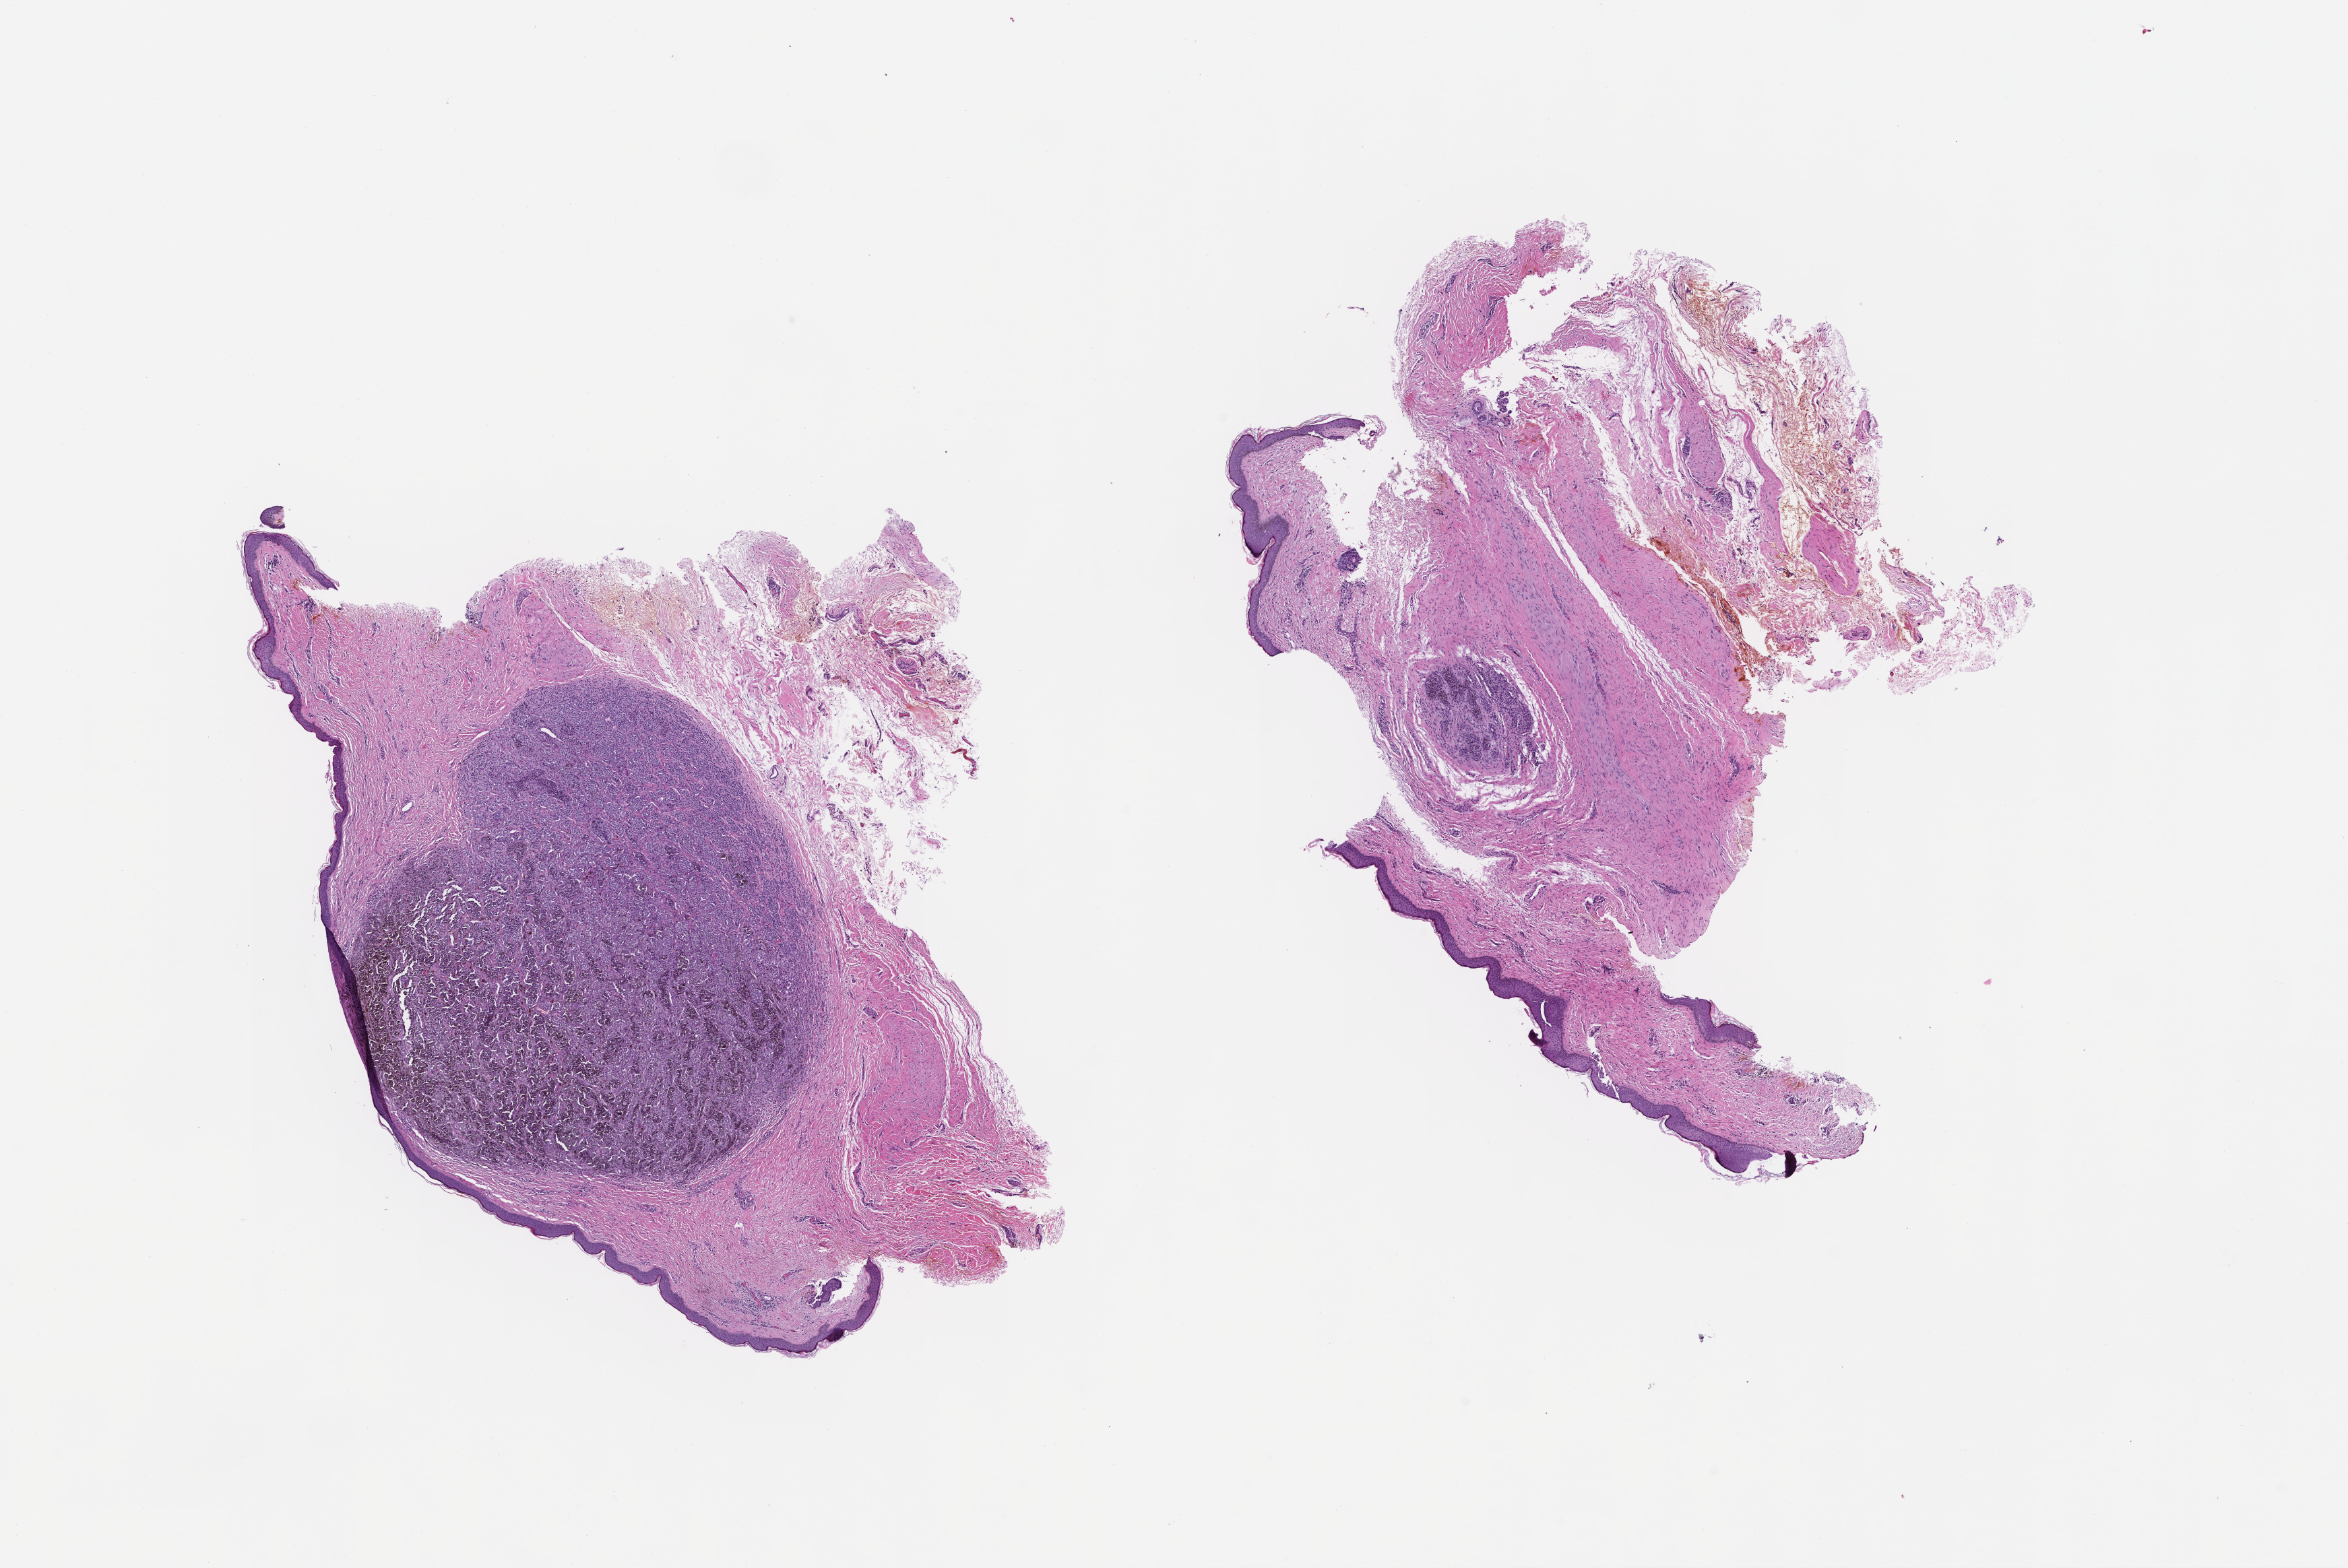
Haematoxylin and eosin whole-slide image — whole scanned area (about 14.1 x 9.4 mm) shown as a low-resolution overview. Formalin-fixed, paraffin-embedded (FFPE) tissue. Site: skin. Patient sex: male.
This section: primary tumour tissue. Diagnosis: Melanoma.